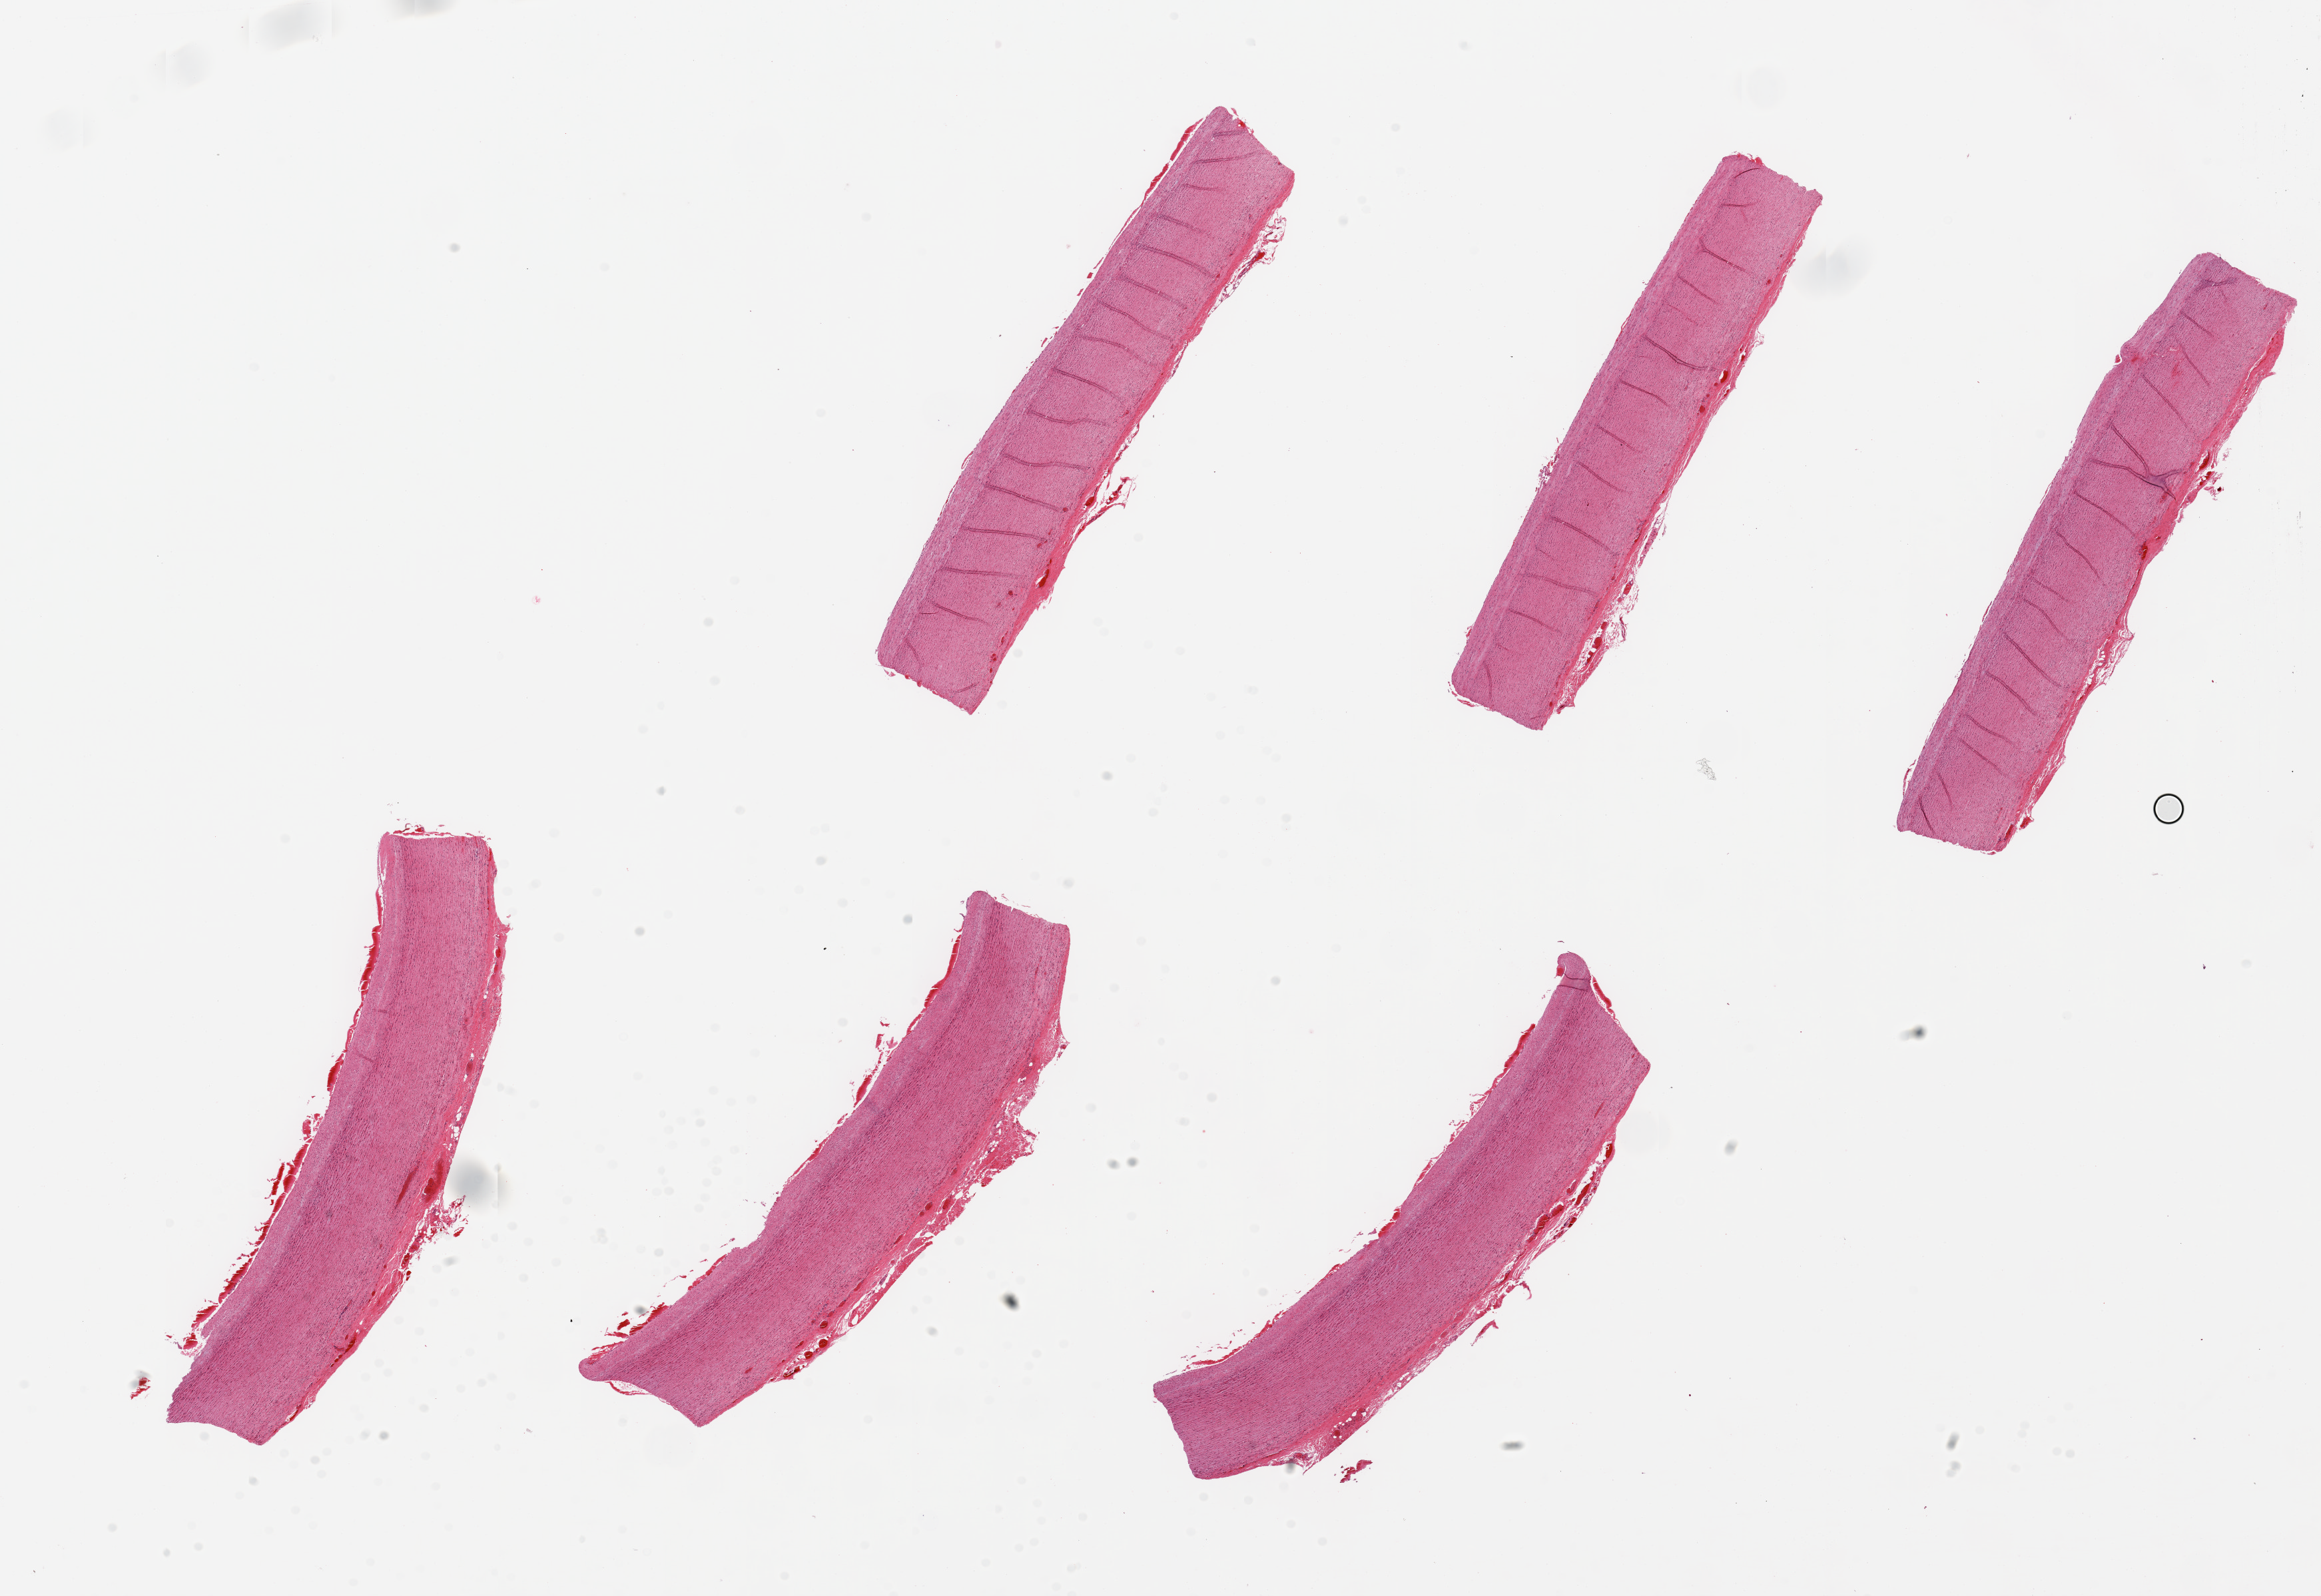
Whole-slide image, H&E stain, brightfield — shown as a low-resolution overview of the whole scanned area (about 27.6 x 19.0 mm, acquisition: 20x scan), PAXgene-fixed, paraffin-embedded tissue, target tissue: aorta, donor tissue sample.
• reviewer comment on this tissue sample: 6 pieces ~7x1,5mm